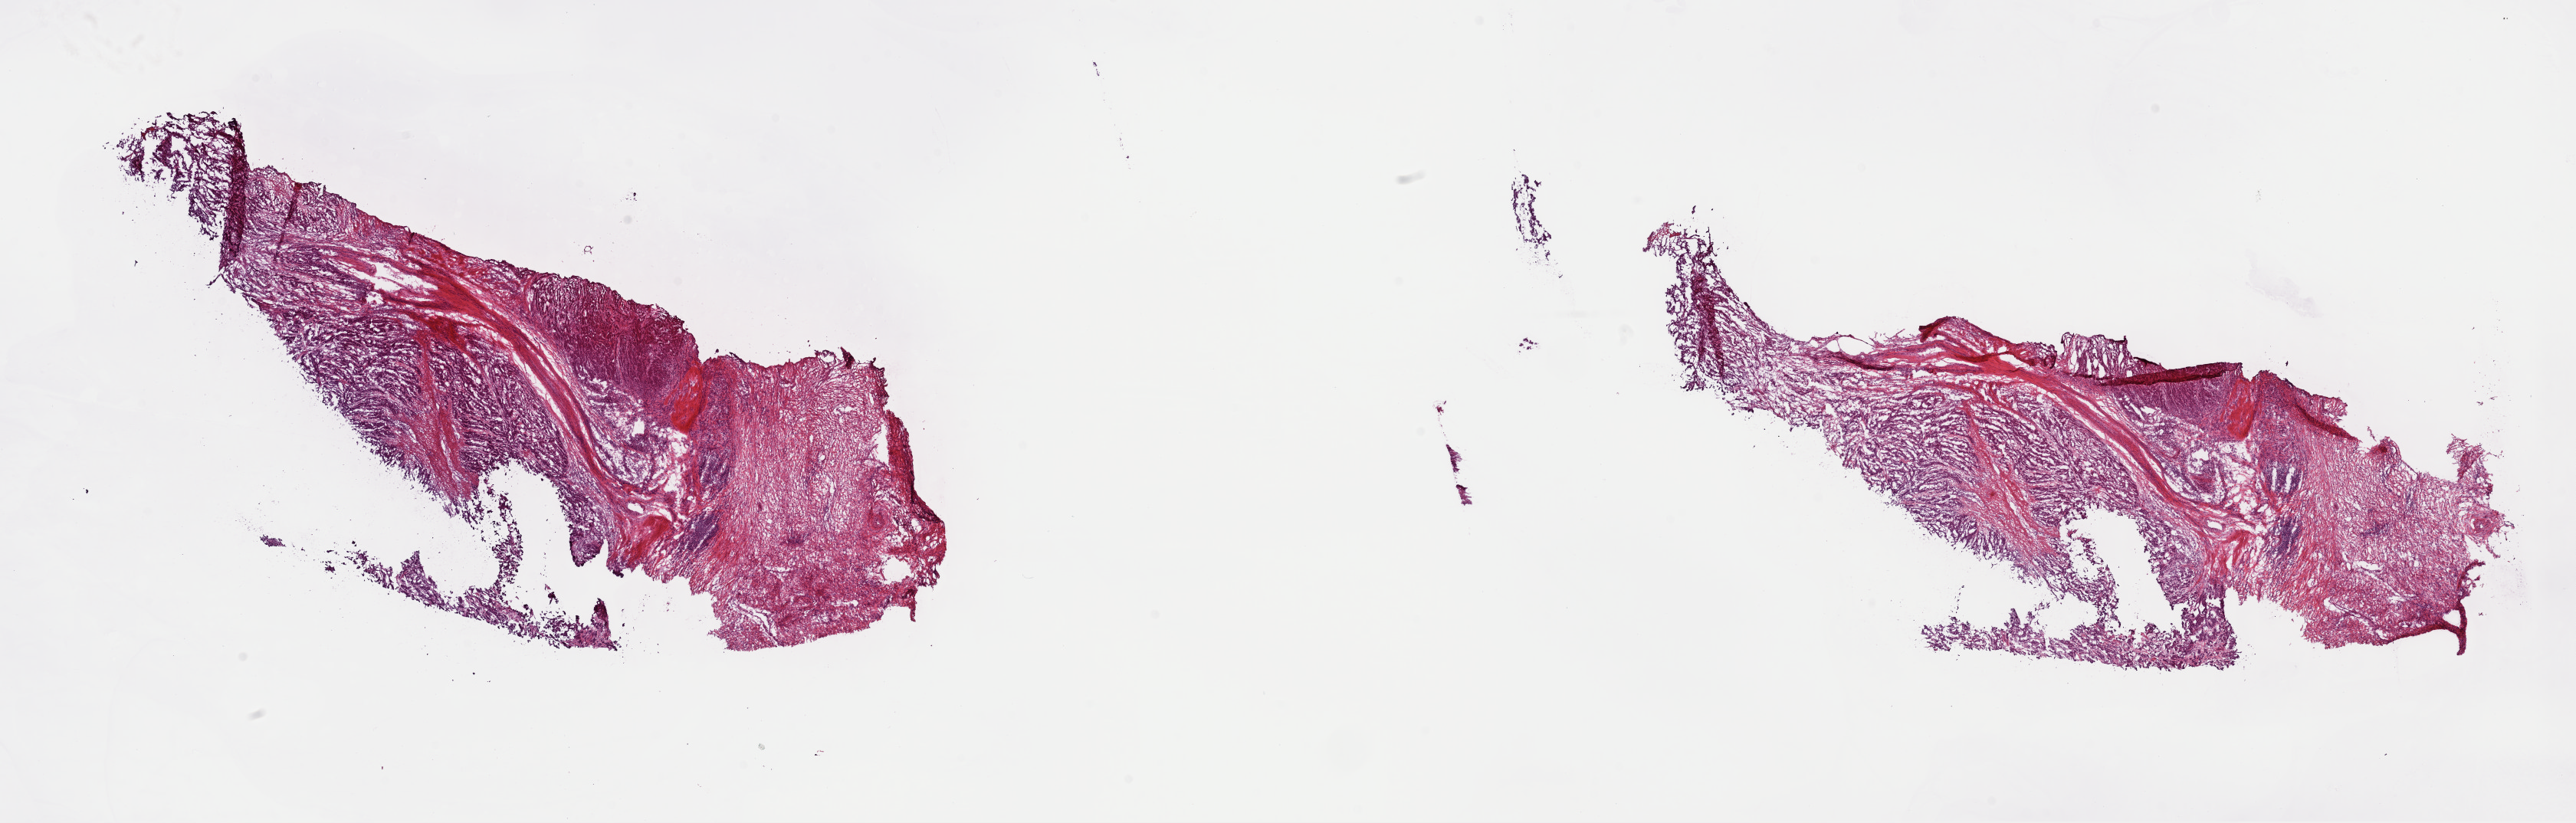
Hematoxylin and eosin (H&E) stained whole-slide image — low-resolution overview of the scanned area, about 26.5 x 8.5 mm (slide scanned at 40x); frozen section from the top of the tissue portion; sample: primary tumour, stomach. Patient: female, age at initial diagnosis 75 years. Histologic grade: G2 (moderately differentiated). Composition of this section per pathologist review: tumour cells 70%, tumour nuclei 60%, normal cells 10%, stromal cells 20%, necrosis 0%. Infiltration values recorded for this section: lymphocyte infiltration 0%, monocyte infiltration 0%, neutrophil infiltration 0%.
- histologic diagnosis: Adenocarcinoma, NOS (gastric antrum)
- lymph nodes positive (case pathology): 9 of 10 examined
- TNM: T3 N3a M0
- AJCC pathologic stage: IIIB (7th edition)